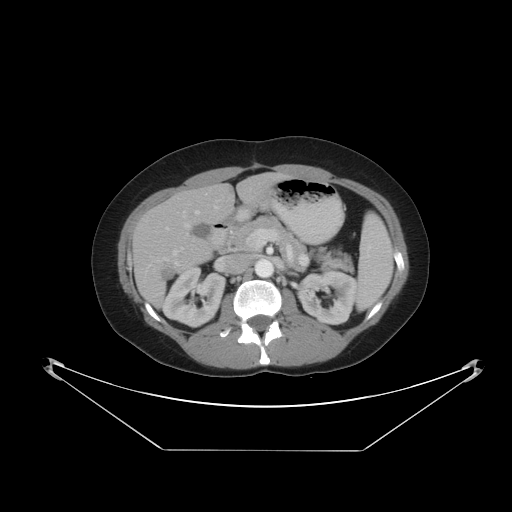
Contrast-enhanced abdominal CT, one axial slice; position 23 of 48 along the scan axis; reconstruction kernel STANDARD; 120 kVp; intravenous contrast given; soft-tissue window (W 400 / L 40 HU); 5 mm slice thickness; 512 × 512 image matrix, field of view 482 × 482 mm. Female patient, age 38 years. Case-level facts recorded for this patient, not image findings: diagnosis: colorectal cancer liver metastases, imaged before liver resection.
Annotated regions visible in this slice (manually delineated by an expert):
- hepatic veins: bounding box [x1, y1, x2, y2] px = [184, 210, 200, 228]
- liver: [133, 176, 283, 306]
- planned liver remnant (the part of the liver to remain after resection): [168, 176, 282, 224]
- portal vein (with intrahepatic branches): [164, 207, 218, 265]
- liver metastasis: [161, 262, 181, 285]